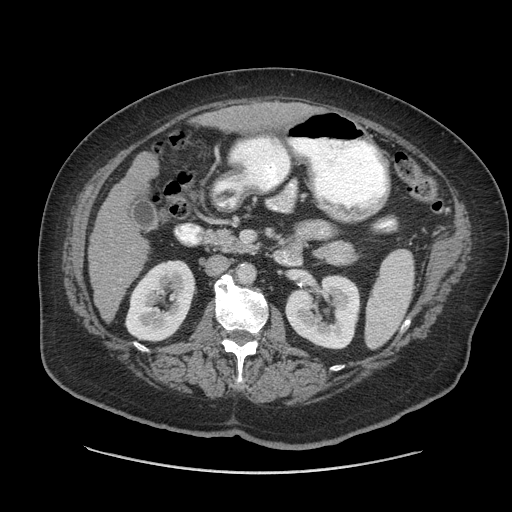
Contrast-enhanced abdominal CT (liver protocol), one axial slice. Slice 23 of 91 in the series (ordered by position). 140 kVp. Soft-tissue window (W 400 / L 40 HU). 2.5 mm slice thickness. 512 × 512 image matrix, field of view 420 × 420 mm. From the clinical record (not read from this slice): diagnosis: hepatocellular carcinoma (patient treated with transarterial chemoembolisation; whether this scan precedes or follows treatment is not stated here); TNM stage (as recorded): Stage-I; Child-Pugh class: A; tumour differentiation: well differentiated; tumour nodularity: uninodular.
Annotated regions visible in this slice (semi-automatic segmentation, software-assisted and operator-edited):
- liver parenchyma outside the tumour (the mass and vessels are separate outlines, so this box may not span the whole liver): box from (x=88, y=104) to (x=310, y=320) px